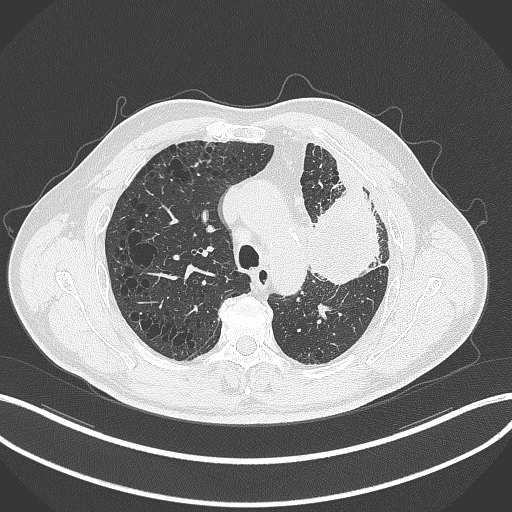
Chest CT, one axial slice. Position 222 of 297 along the scan axis. Reconstruction kernel B70f. 120 kVp. Lung window (W 1500 / L -600 HU). 512 × 512 image matrix. Male patient, age 68 years. Case-level facts recorded for this patient, not image findings: clinical TNM (as recorded): T3 N3 M1.
Structures marked on this image (rectangle marked by the reading radiologist):
- lung tumour (recorded histology: adenocarcinoma): bounding box [x1, y1, x2, y2] px = [301, 184, 382, 289]